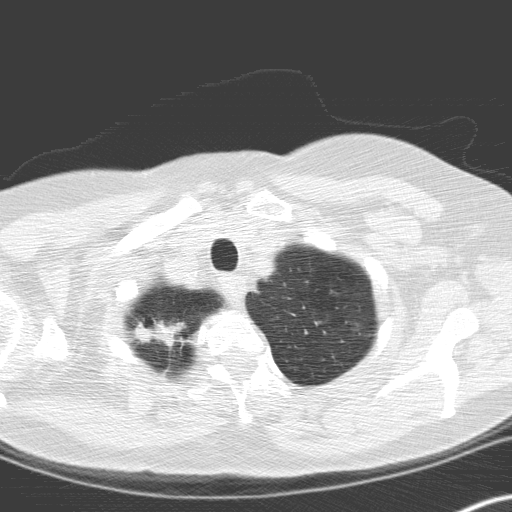
Axial slice from a low-dose chest CT screening exam. Second screening round (one year after baseline). Lung window (W 1500 / L -600 HU). 3.2 mm slice thickness. Standard (soft-tissue) reconstruction kernel (C). 120 kVp. Slice 23 of 166 in the series. 512 × 512 image matrix. Female participant, aged 60 years at enrolment. Current smoker at enrolment.
• Lesion marked by an expert reader, bounding box [x1, y1, x2, y2] px = [127, 308, 200, 373].
• The exam's reader record, not a measurement of the box and not confirmed to be the same lesion: non-calcified nodule or mass ≥4 mm, right upper lobe, 12 × 8 mm, spiculated (stellate) margins, soft tissue attenuation, pre-existing on the prior screen: no.
• Official screen result: positive, other.
• Later outcome: lung cancer diagnosed 58 days after this screen — squamous cell carcinoma, keratinizing, NOS, right upper lobe, moderately differentiated (G2), stage IA (AJCC 6th edition), 20 mm at pathology.